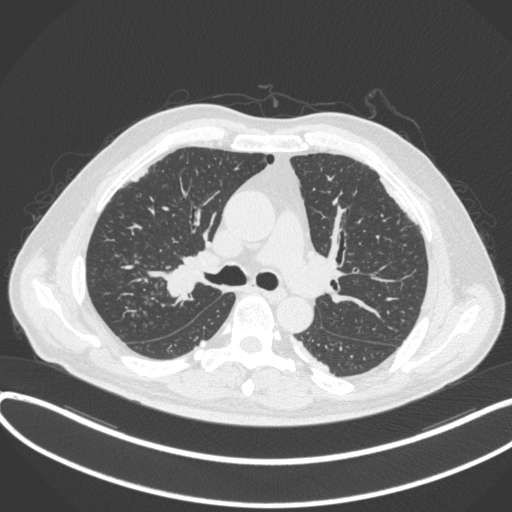
Chest CT, one axial slice. Slice 267 of 455 in the series (ordered by position). Reconstruction kernel B31f. 120 kVp. Lung window (W 1500 / L -600 HU). 512 × 512 image matrix, field of view 400 × 400 mm. Patient: male, 58 years. From the clinical record (not read from this slice): clinical TNM (as recorded): T1c N0 M0.
Outlined on this slice (bounding box drawn by a radiologist):
- lung tumour (recorded histology: squamous cell carcinoma): bounding box [x1, y1, x2, y2] px = [149, 259, 207, 298]